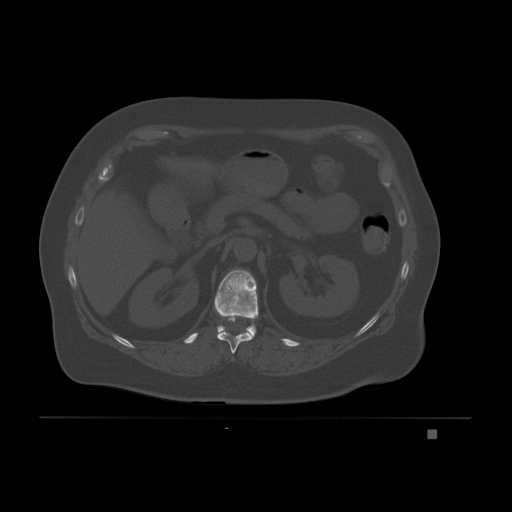
CT including the spine, one axial slice; position 85 of 221 along the scan axis; bone window (W 1800 / L 400 HU); 3 mm slice thickness; 512 × 512 image matrix, field of view 474 × 474 mm. Patient: female, 63 years. Case-level facts recorded for this patient, not image findings: primary cancer: breast.
Outlined on this slice (semi-automatic segmentation, software-assisted and operator-edited):
- T11 vertebra: bounding box [x1, y1, x2, y2] px = [217, 319, 253, 354]
- T12 vertebra: [214, 269, 259, 337]